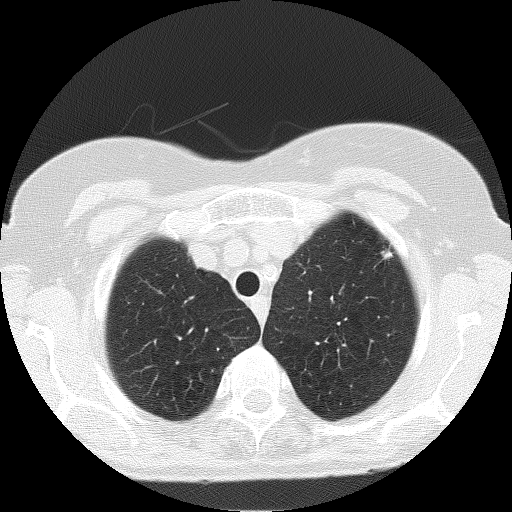
Low-dose screening chest CT, one axial slice; position 143 of 166 along the scan axis; reconstruction kernel FC51; lung window (W 1500 / L -600 HU); 512 × 512 image matrix, field of view 303 × 303 mm.
Structures marked on this image (manually delineated by an expert):
- lesion 4 (nodule, upper lobe of left lung): bounding box <381,250,393,260> (left, top, right, bottom; pixels)